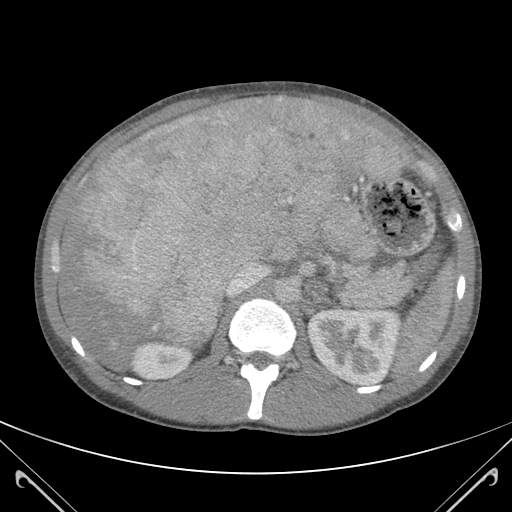
Contrast-enhanced abdominal CT (liver protocol), one axial slice. Slice 71 of 118 in the series (ordered by position). 120 kVp. Soft-tissue window (W 400 / L 40 HU). 512 × 512 image matrix, field of view 380 × 380 mm. From the clinical record (not read from this slice): diagnosis: hepatocellular carcinoma (patient treated with transarterial chemoembolisation; whether this scan precedes or follows treatment is not stated here); TNM stage (as recorded): Stage-IIIB; Child-Pugh class: A; tumour nodularity: uninodular.
Structures marked on this image (semi-automatic segmentation, software-assisted and operator-edited):
- abdominal aorta: bounding box <276,278,298,302> (left, top, right, bottom; pixels)
- liver parenchyma outside the tumour (the mass and vessels are separate outlines, so this box may not span the whole liver): <58,97,398,367>
- mass: <65,98,384,343>
- liver vessels: <223,98,395,296>